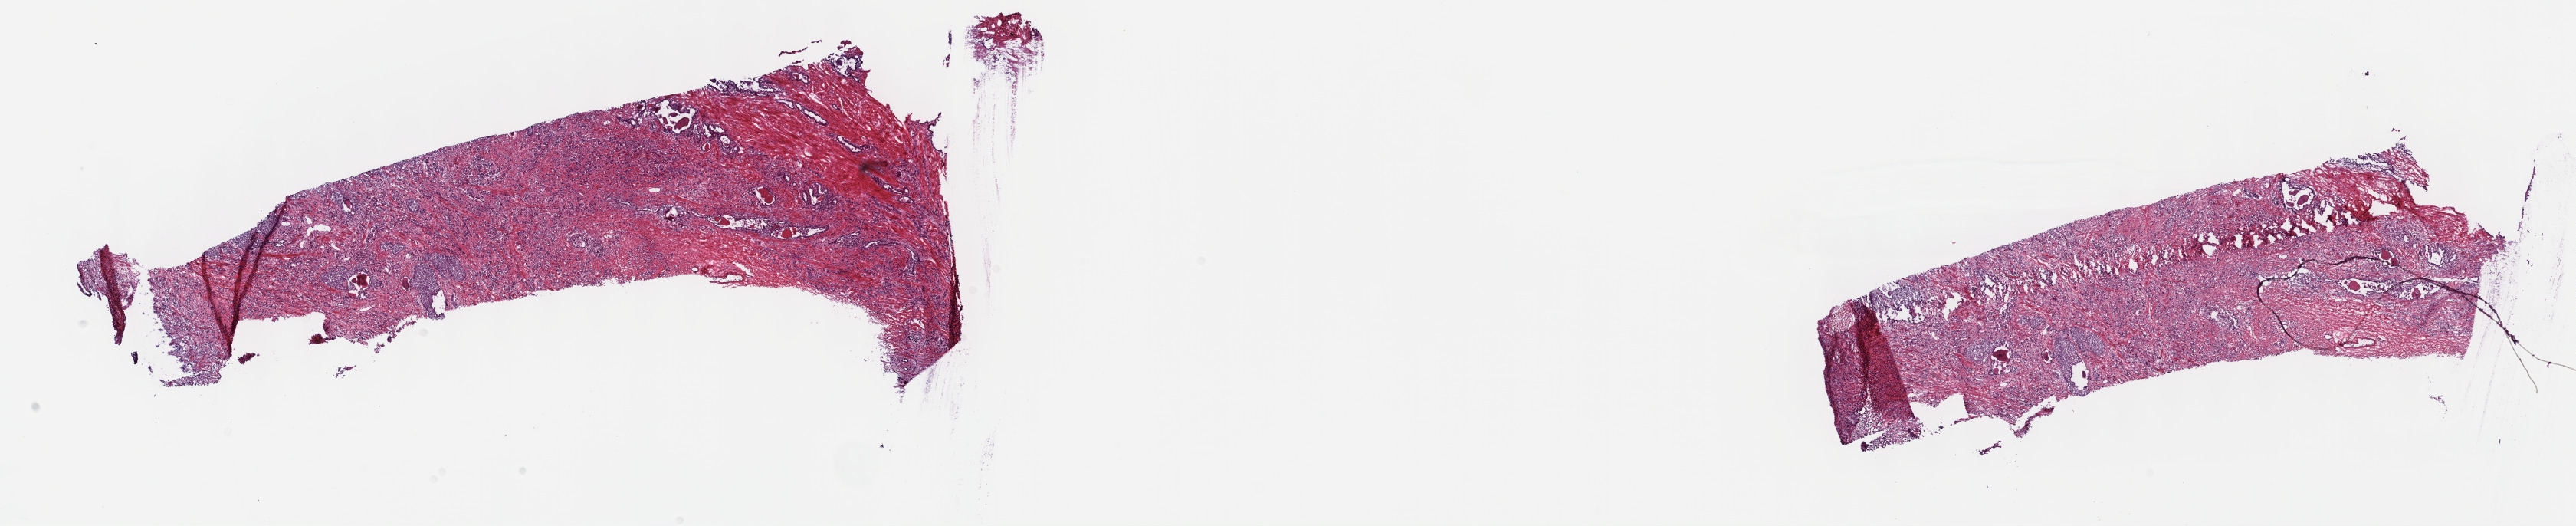
Whole-slide histology image, Hematoxylin and eosin (H&E) stained — shown as a low-resolution overview of the whole scanned area (about 27.2 x 5.5 mm). Frozen section from the top of the tissue portion. Sample: primary tumour, prostate. Male, age 57 years at initial diagnosis.
Diagnosis: Adenocarcinoma, NOS.